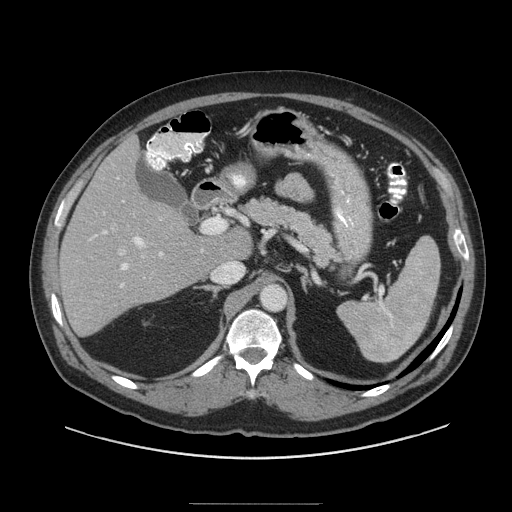
Contrast-enhanced abdominal CT (liver protocol), one axial slice; position 57 of 91 along the scan axis; reconstruction kernel STANDARD; soft-tissue window (W 400 / L 40 HU); 2.5 mm slice thickness; 512 × 512 image matrix, field of view 440 × 440 mm. Case-level facts recorded for this patient, not image findings: diagnosis: hepatocellular carcinoma (patient treated with transarterial chemoembolisation; whether this scan precedes or follows treatment is not stated here); TNM stage (as recorded): Stage-I; Child-Pugh class: A; tumour differentiation: well differentiated; tumour size: 4 cm.
Annotated regions visible in this slice (semi-automatic segmentation, software-assisted and operator-edited):
- liver parenchyma outside the tumour (the mass and vessels are separate outlines, so this box may not span the whole liver): box from (x=58, y=136) to (x=239, y=336) px
- liver vessels: (x=90, y=178)–(x=163, y=288)